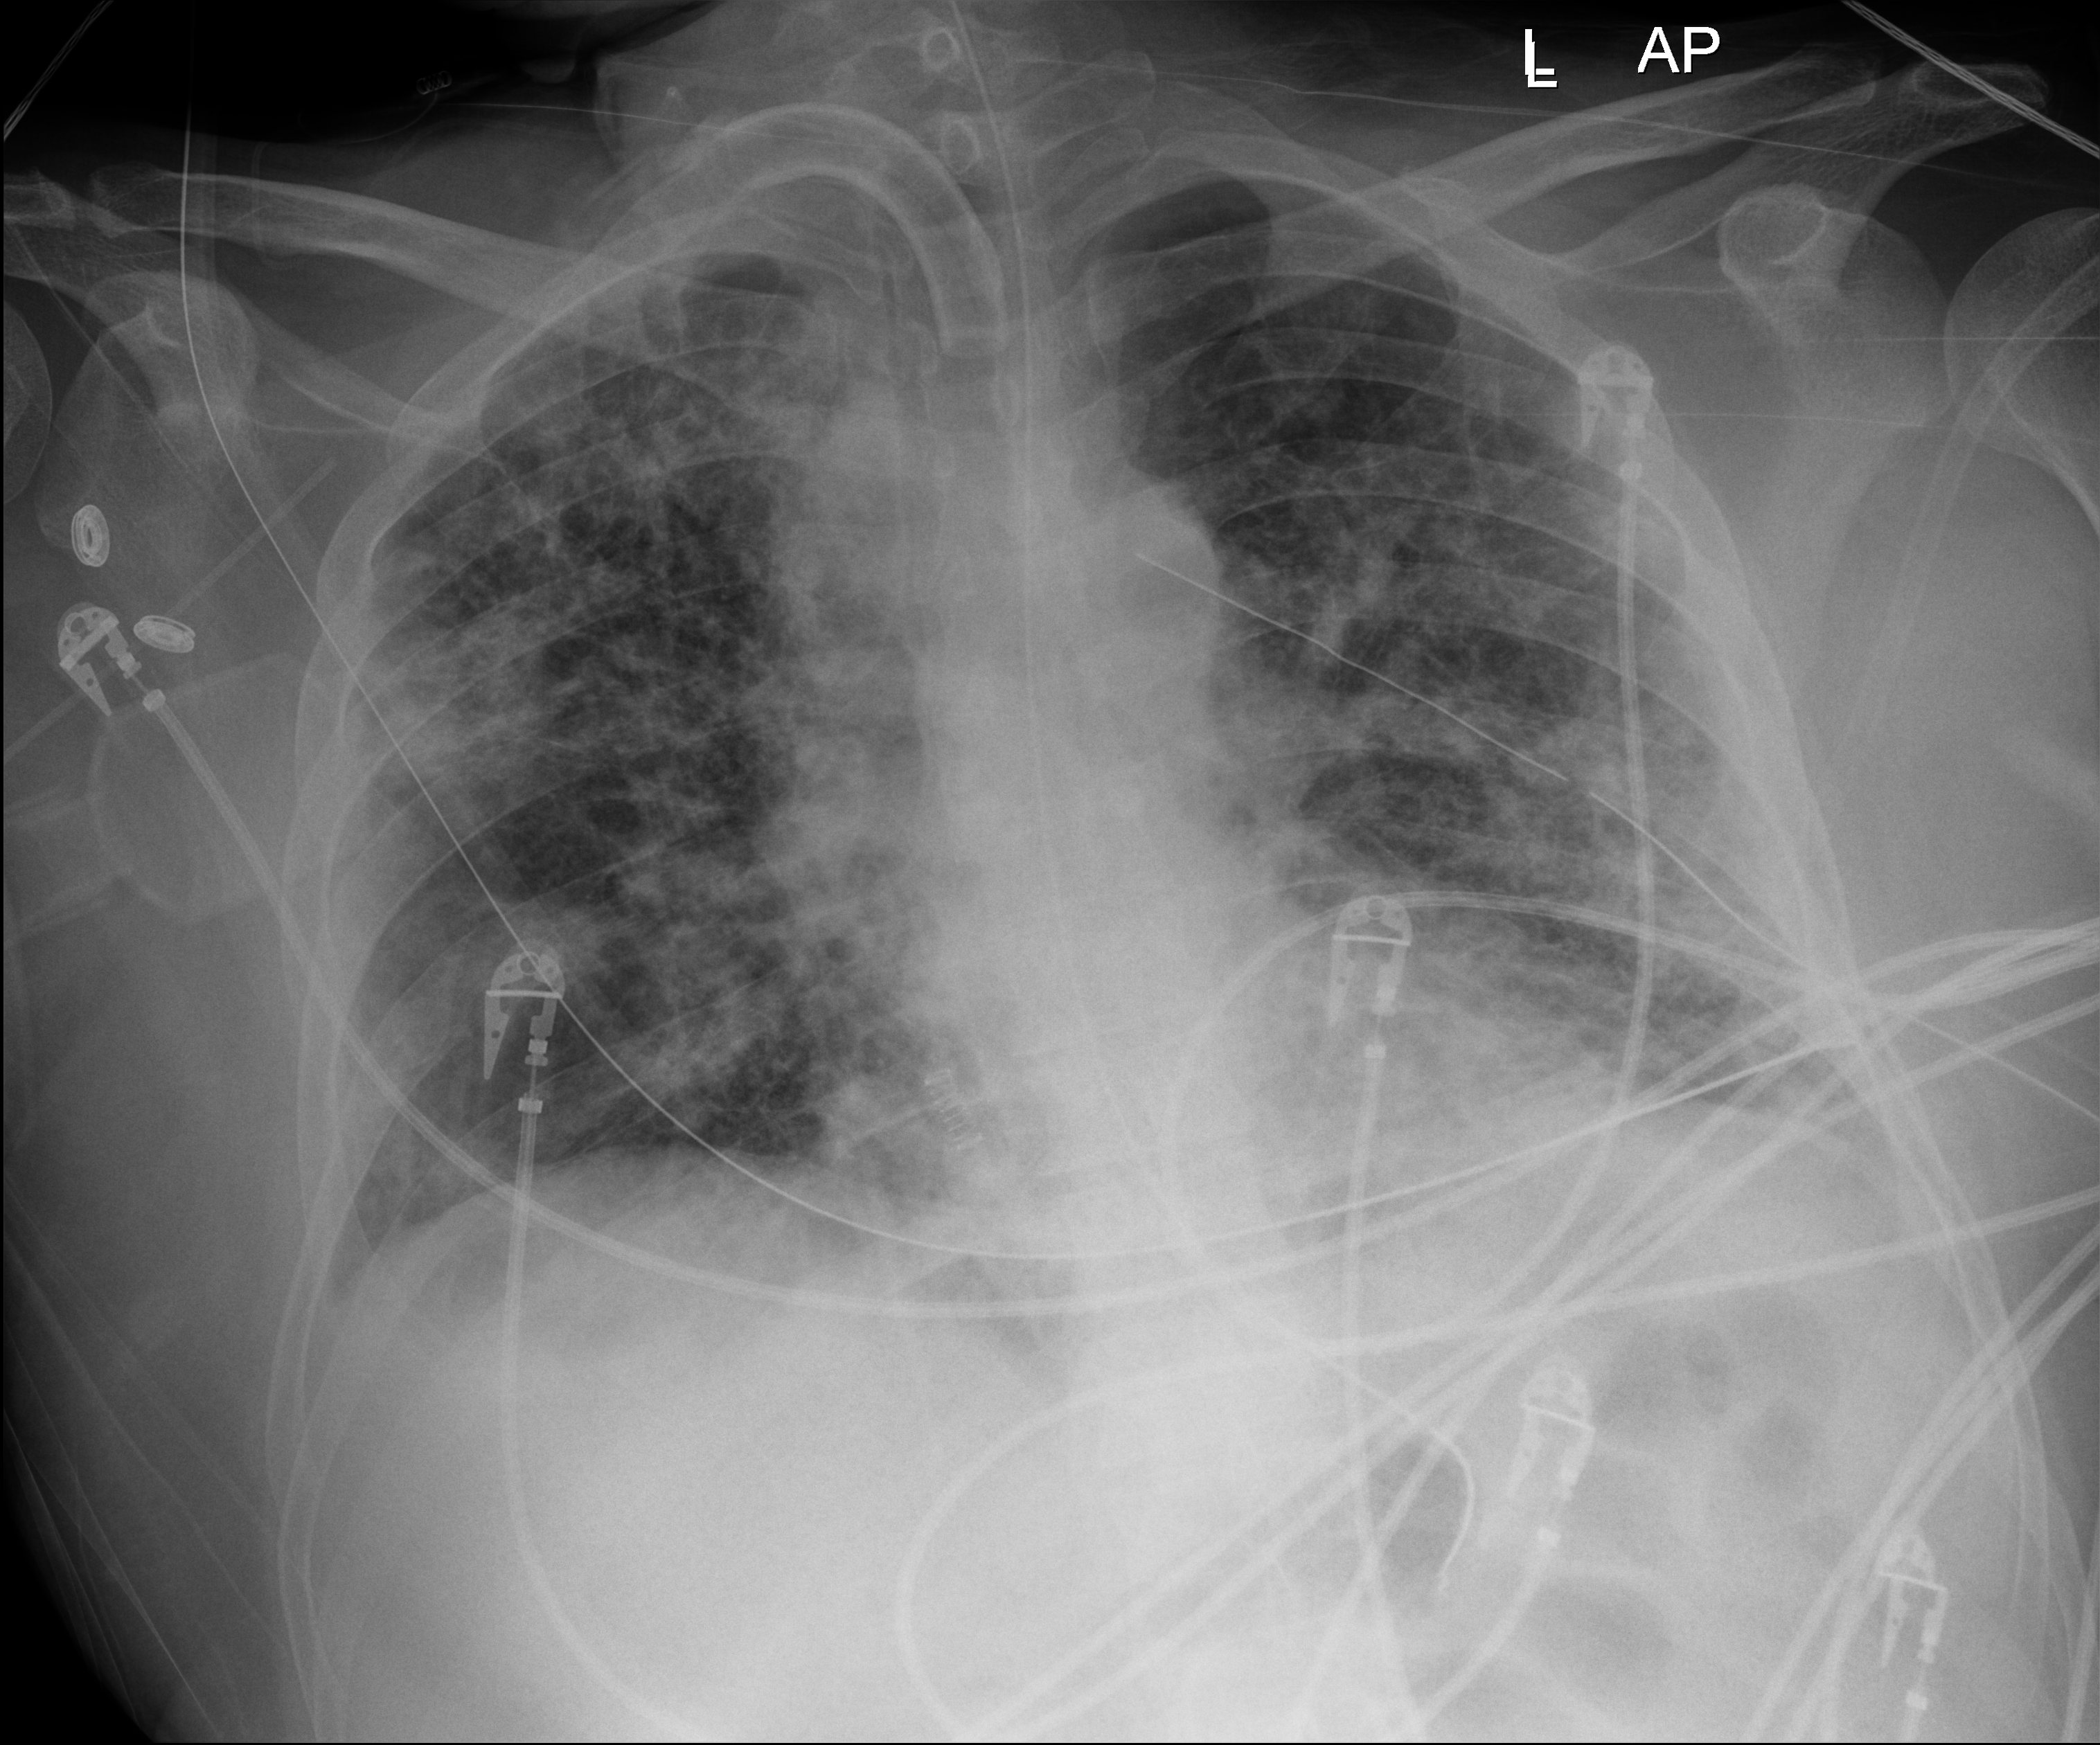
Chest radiograph (digital radiography); anteroposterior (AP) projection. Male patient hospitalised with COVID-19, age 18–59 years.
Hospital-stay facts (about this admission, not read from this image; timing relative to this image not recorded): mechanically ventilated during this hospital stay: yes; other chronic lung disease (admission record): no; admitted to intensive care during this hospital stay: yes.